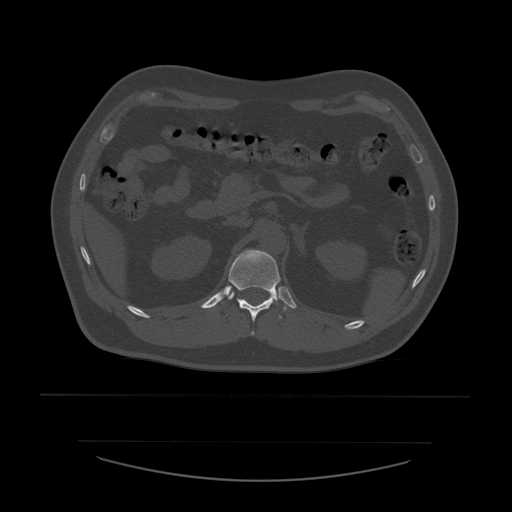
CT including the spine, one axial slice. Slice 248 of 532 in the series (ordered by position). Reconstruction kernel STANDARD. Bone window (W 1800 / L 400 HU). 512 × 512 image matrix, field of view 441 × 441 mm. Patient age 44 years. From the clinical record (not read from this slice): primary cancer: soft tissue sarcoma.
Outlined on this slice (semi-automatic segmentation, software-assisted and operator-edited):
- T12 vertebra: bounding box [x1, y1, x2, y2] px = [229, 250, 287, 335]